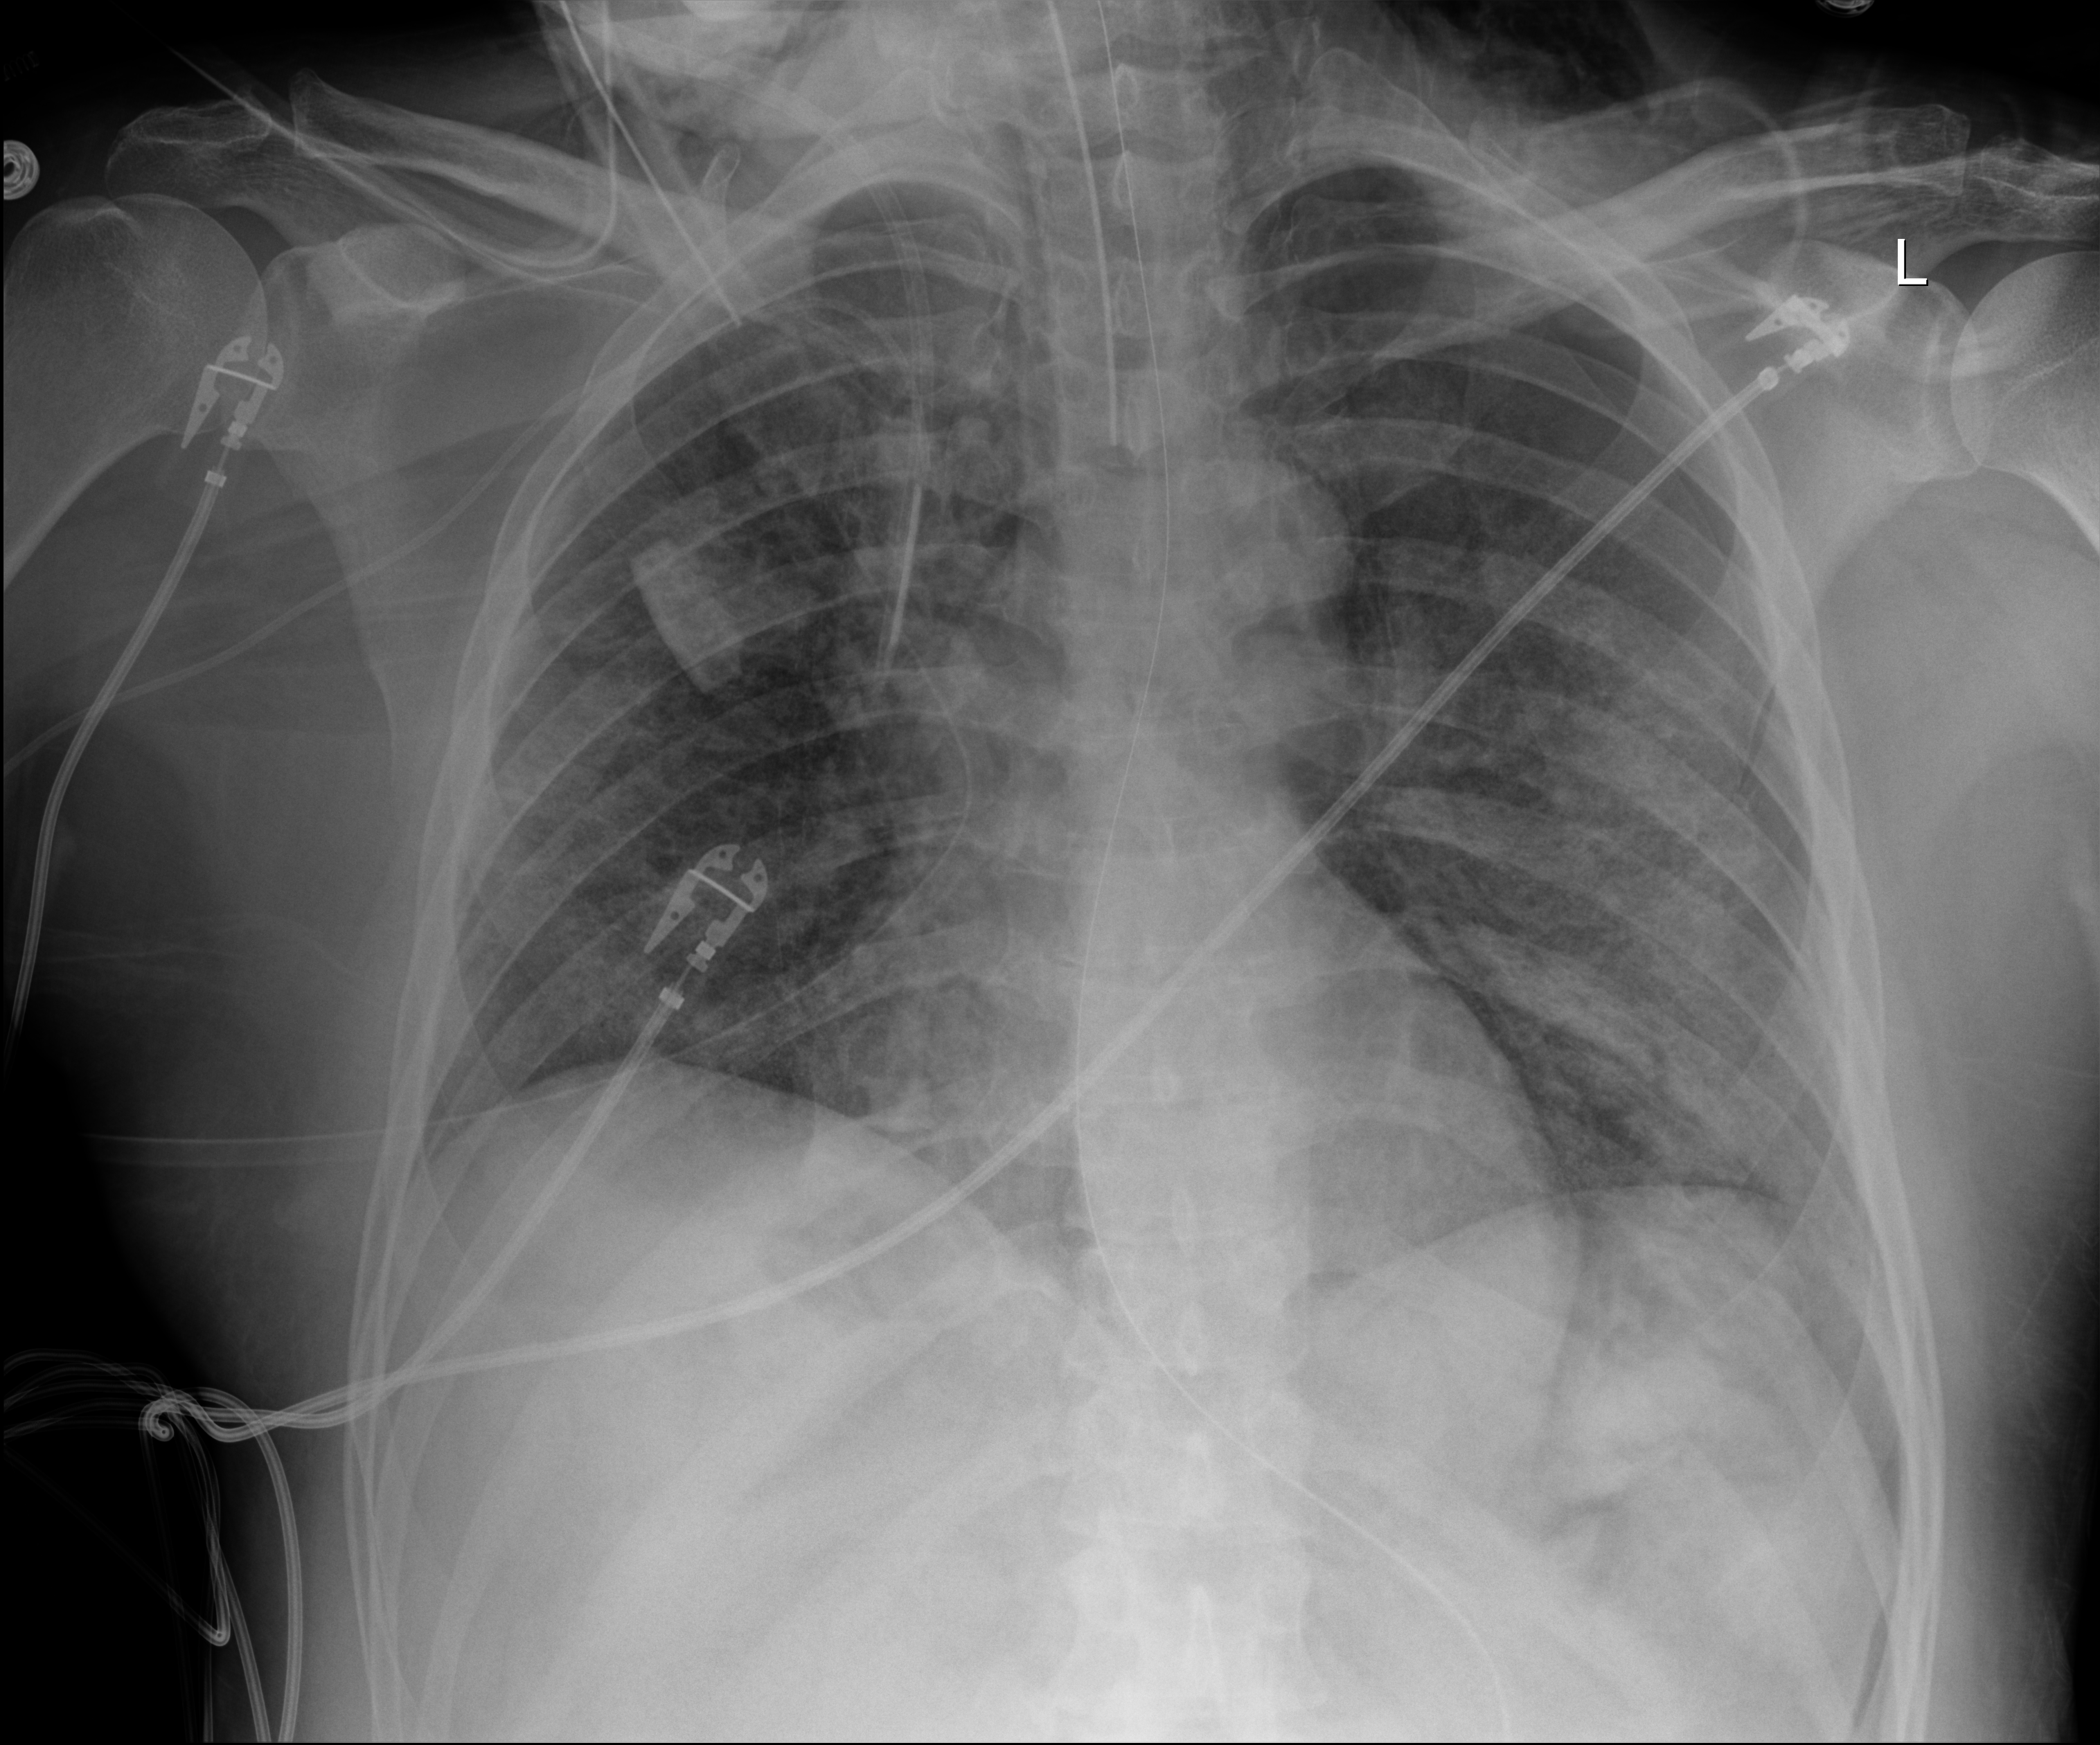
Portable chest radiograph; anteroposterior (AP) projection. Male patient hospitalised with COVID-19, age 18–59 years.
Hospital-stay facts (about this admission, not read from this image; timing relative to this image not recorded):
- admitted to intensive care during this hospital stay: yes
- length of hospital stay: 77 days
- diabetes (admission record): no